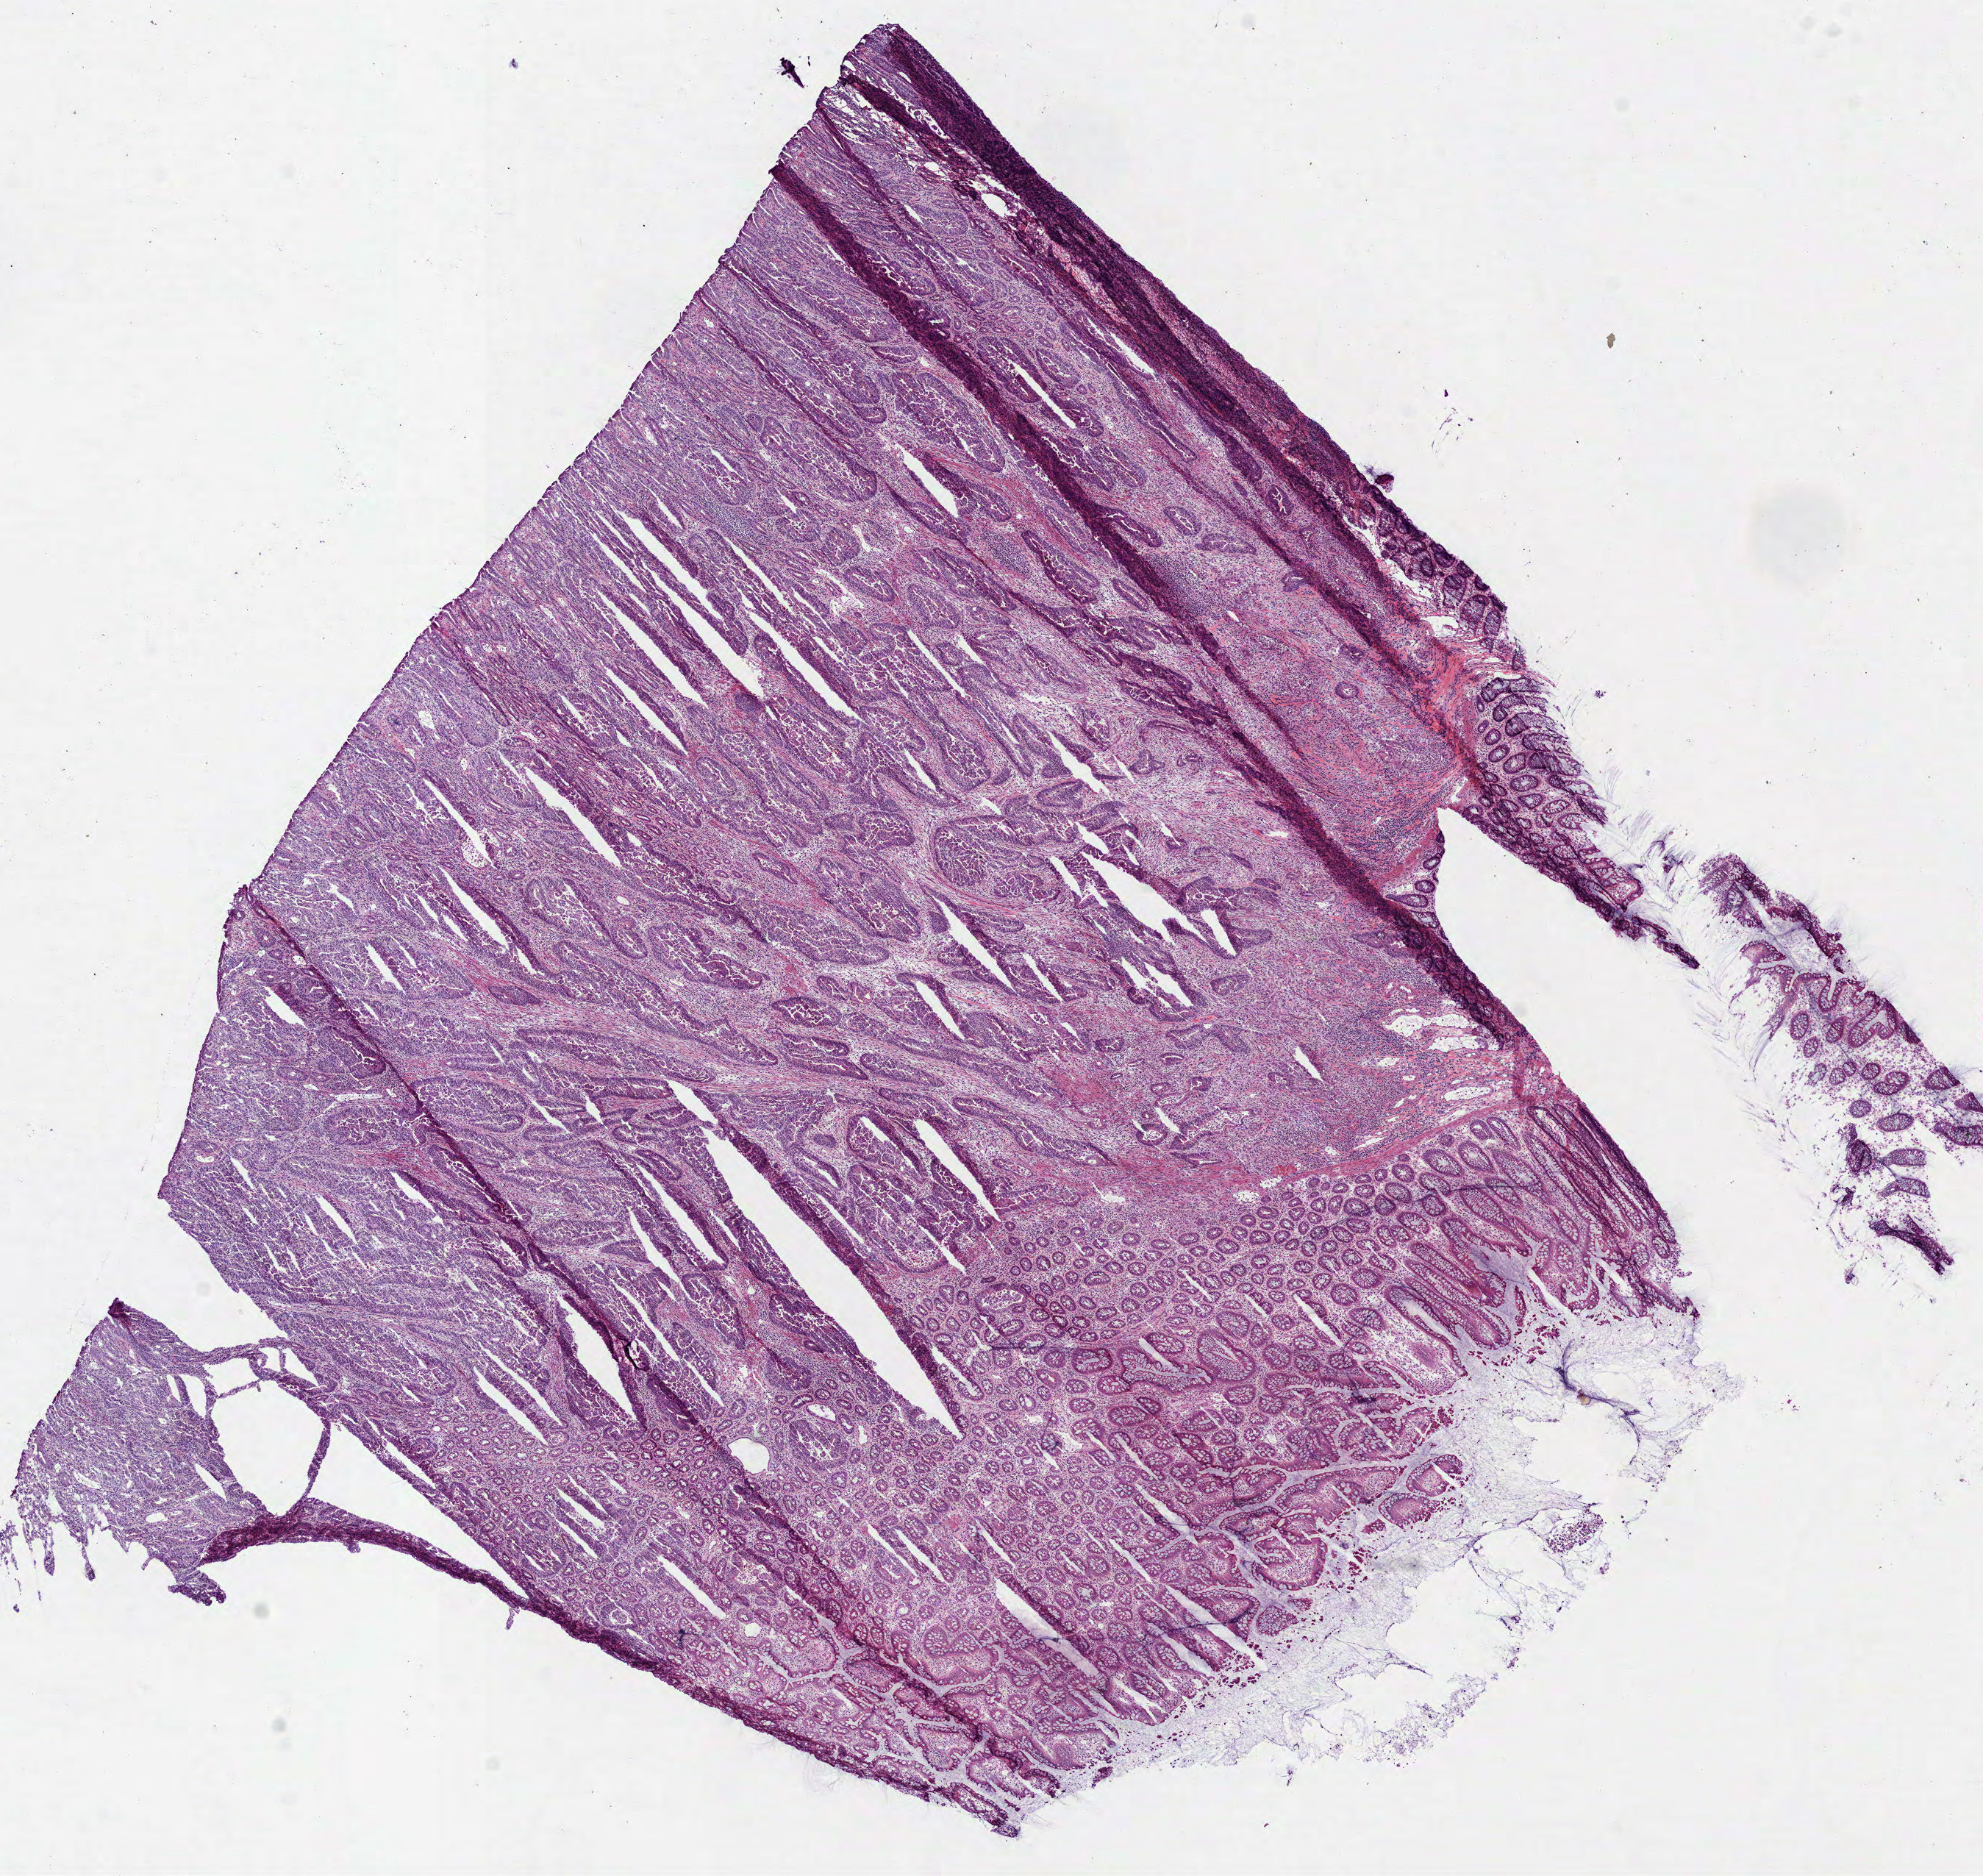
Whole-slide histology image, Hematoxylin and eosin (H&E) stained — shown as a low-resolution overview of the whole scanned area (about 10.9 x 10.3 mm, slide scanned at 40x). Frozen section from the bottom of the tissue portion. Primary tumour sample from the colon. Female patient; age at initial diagnosis 45 years. Slide review estimates, as recorded: tumour cells 70%, tumour nuclei 71%, normal cells 30%, stromal cells 0%, necrosis 0%. Inflammatory infiltration, as recorded: lymphocyte infiltration 20%, monocyte infiltration 1%, neutrophil infiltration 2%.
Lymph nodes positive (case pathology): 0 of 12 examined. Histologic diagnosis: Adenocarcinoma, NOS (transverse colon).